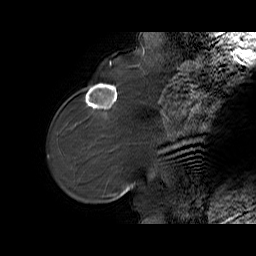
Breast MRI (dynamic contrast-enhanced), one sagittal slice. Slice 18 of 65 in the series (ordered by position). Dynamic contrast-enhanced series, time point 2 of 6 at this slice position (early post-contrast). 1.5 T. TE 5.7 ms, TR 32.9 ms. 256 × 256 image matrix, field of view 230 × 230 mm. Female patient. Case-level facts recorded for this patient, not image findings: setting: breast cancer imaged before/during neoadjuvant chemotherapy; receptor status: HER2-positive.
Annotated regions visible in this slice (semi-automatically segmented with operator editing):
- analysis volume of interest (the breast-tissue region the enhancement analysis was run in; not a lesion): bounding box <76,79,125,128> (left, top, right, bottom; pixels)
- tumour enhancement mask (voxels above the 100 % enhancement threshold inside the analysis volume of interest): <85,83,117,109>